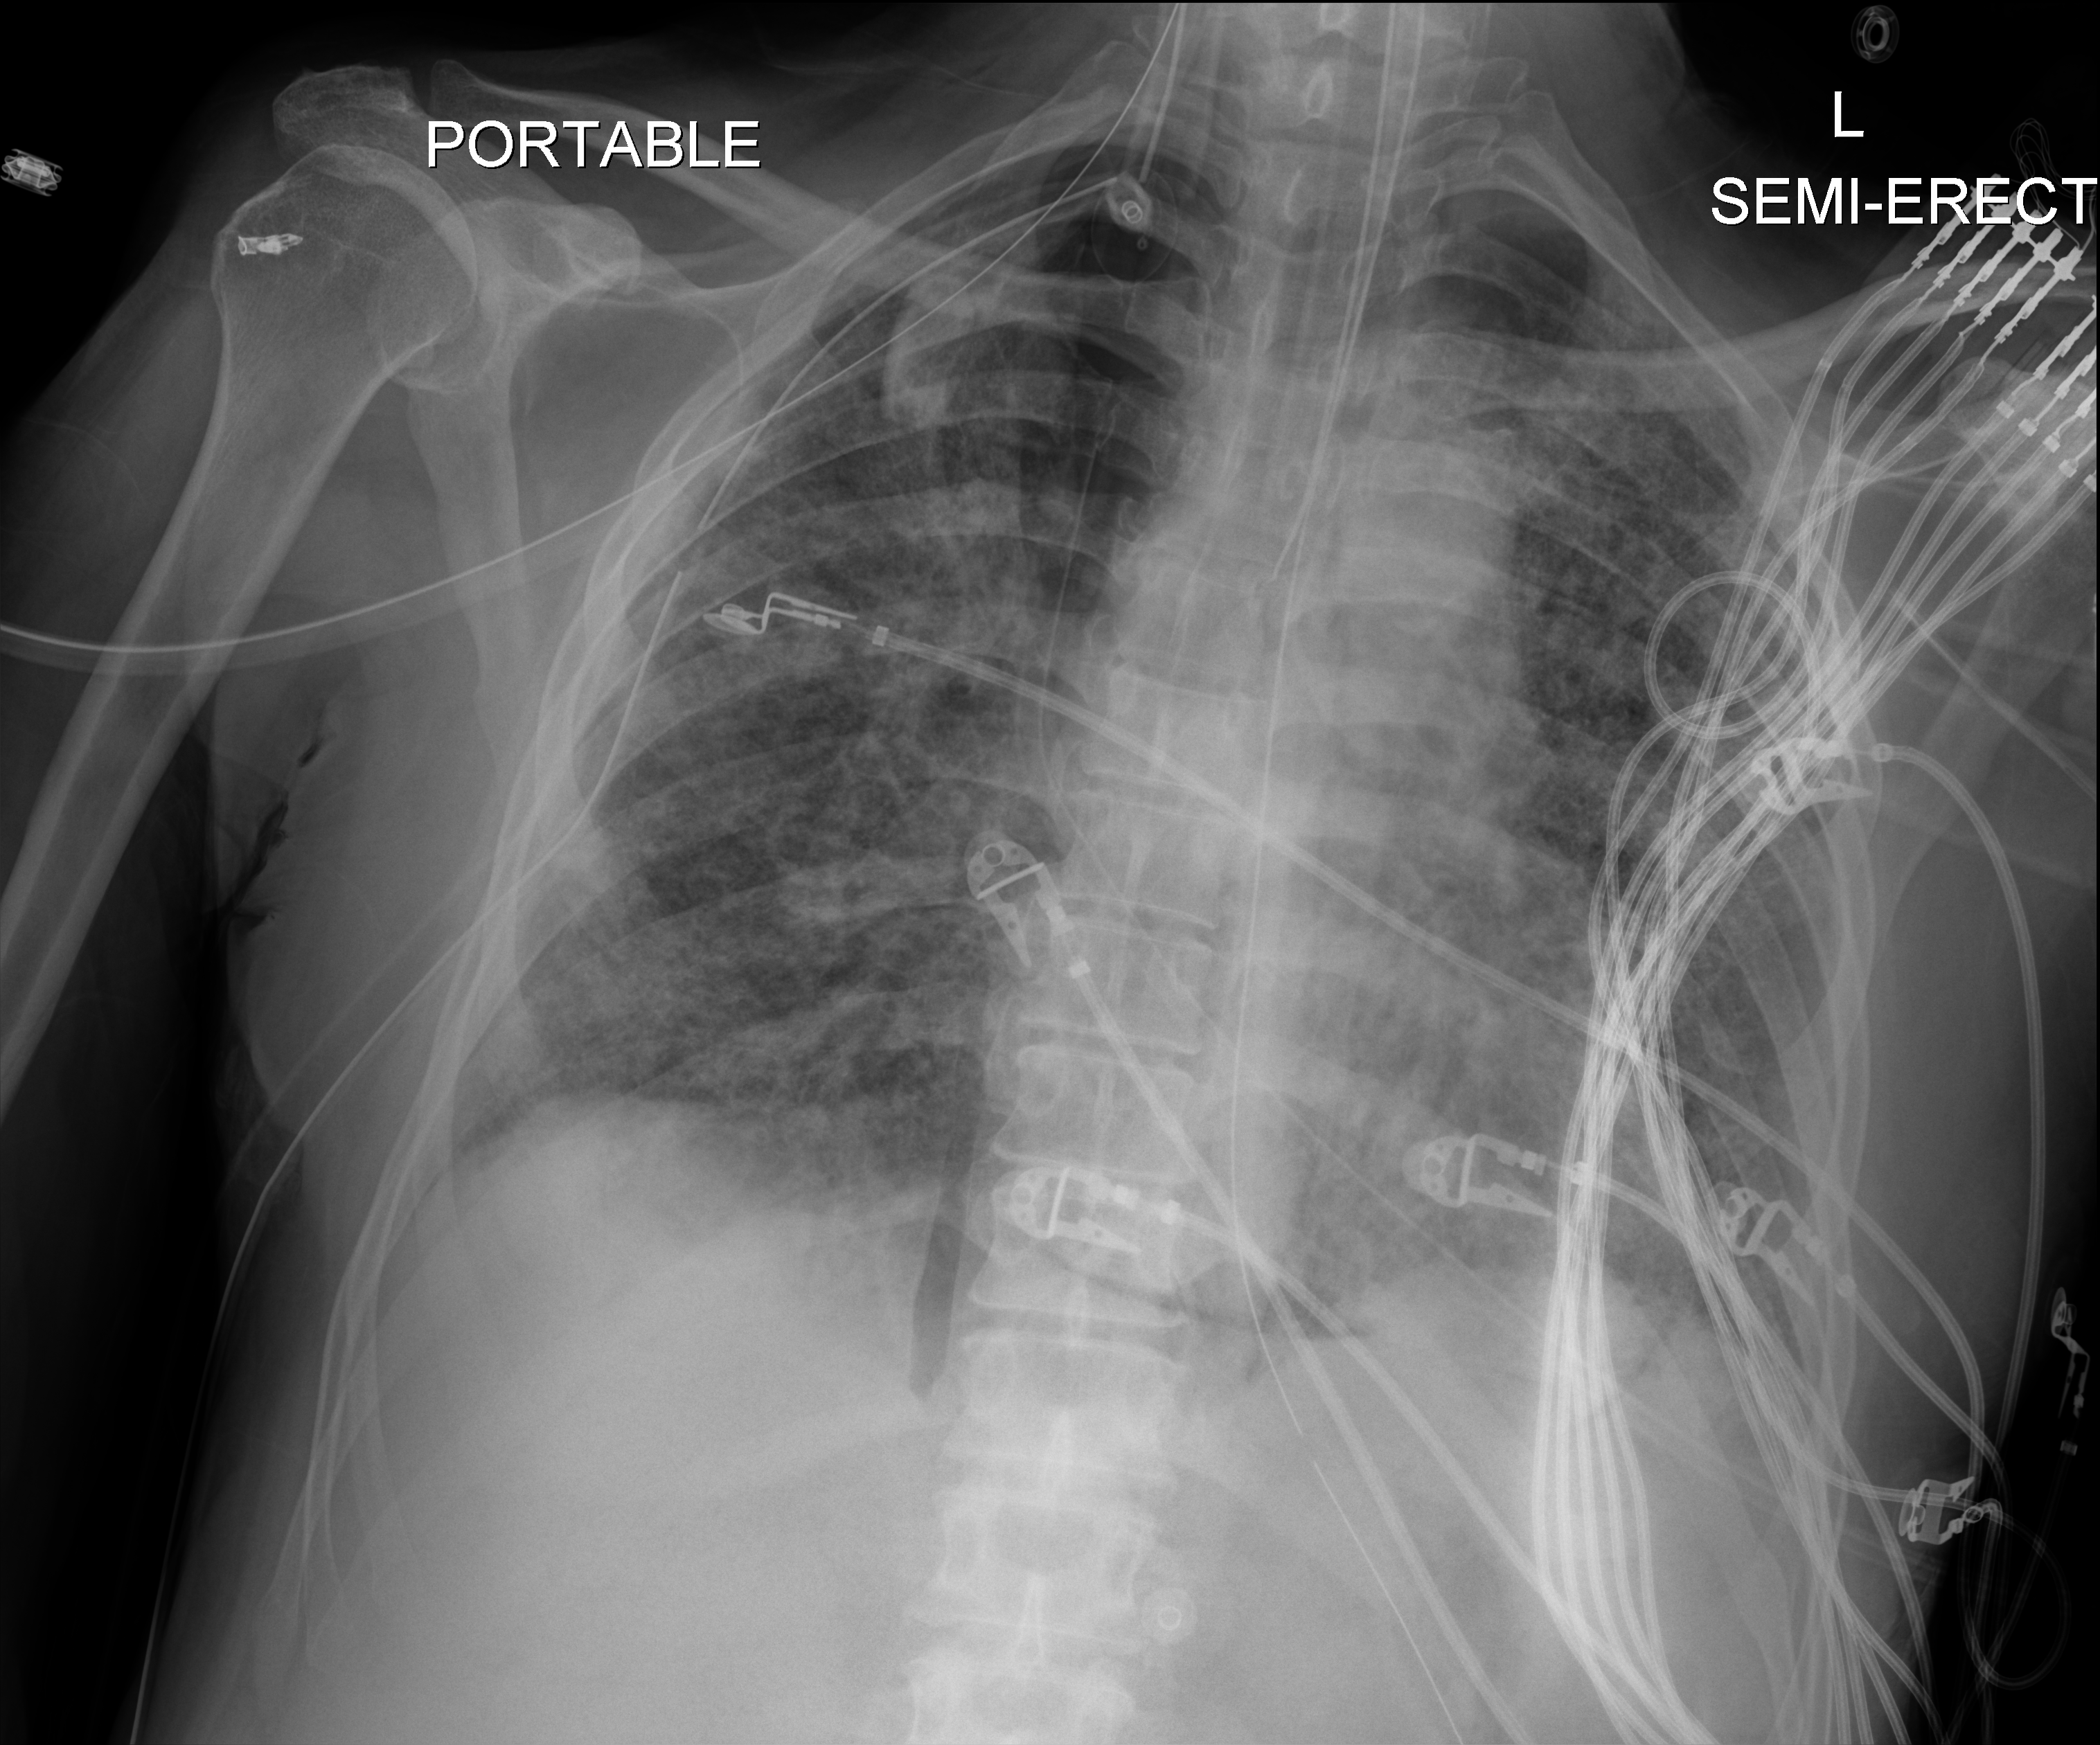
Bedside chest radiograph (digital radiography), anteroposterior (AP) projection. Patient hospitalised with COVID-19; male, aged 60–74 years.
From the hospital-stay record, not from the radiograph (when in the stay this image was taken is not recorded): COPD (admission record): no; other chronic lung disease (admission record): yes; length of hospital stay: 65 days.